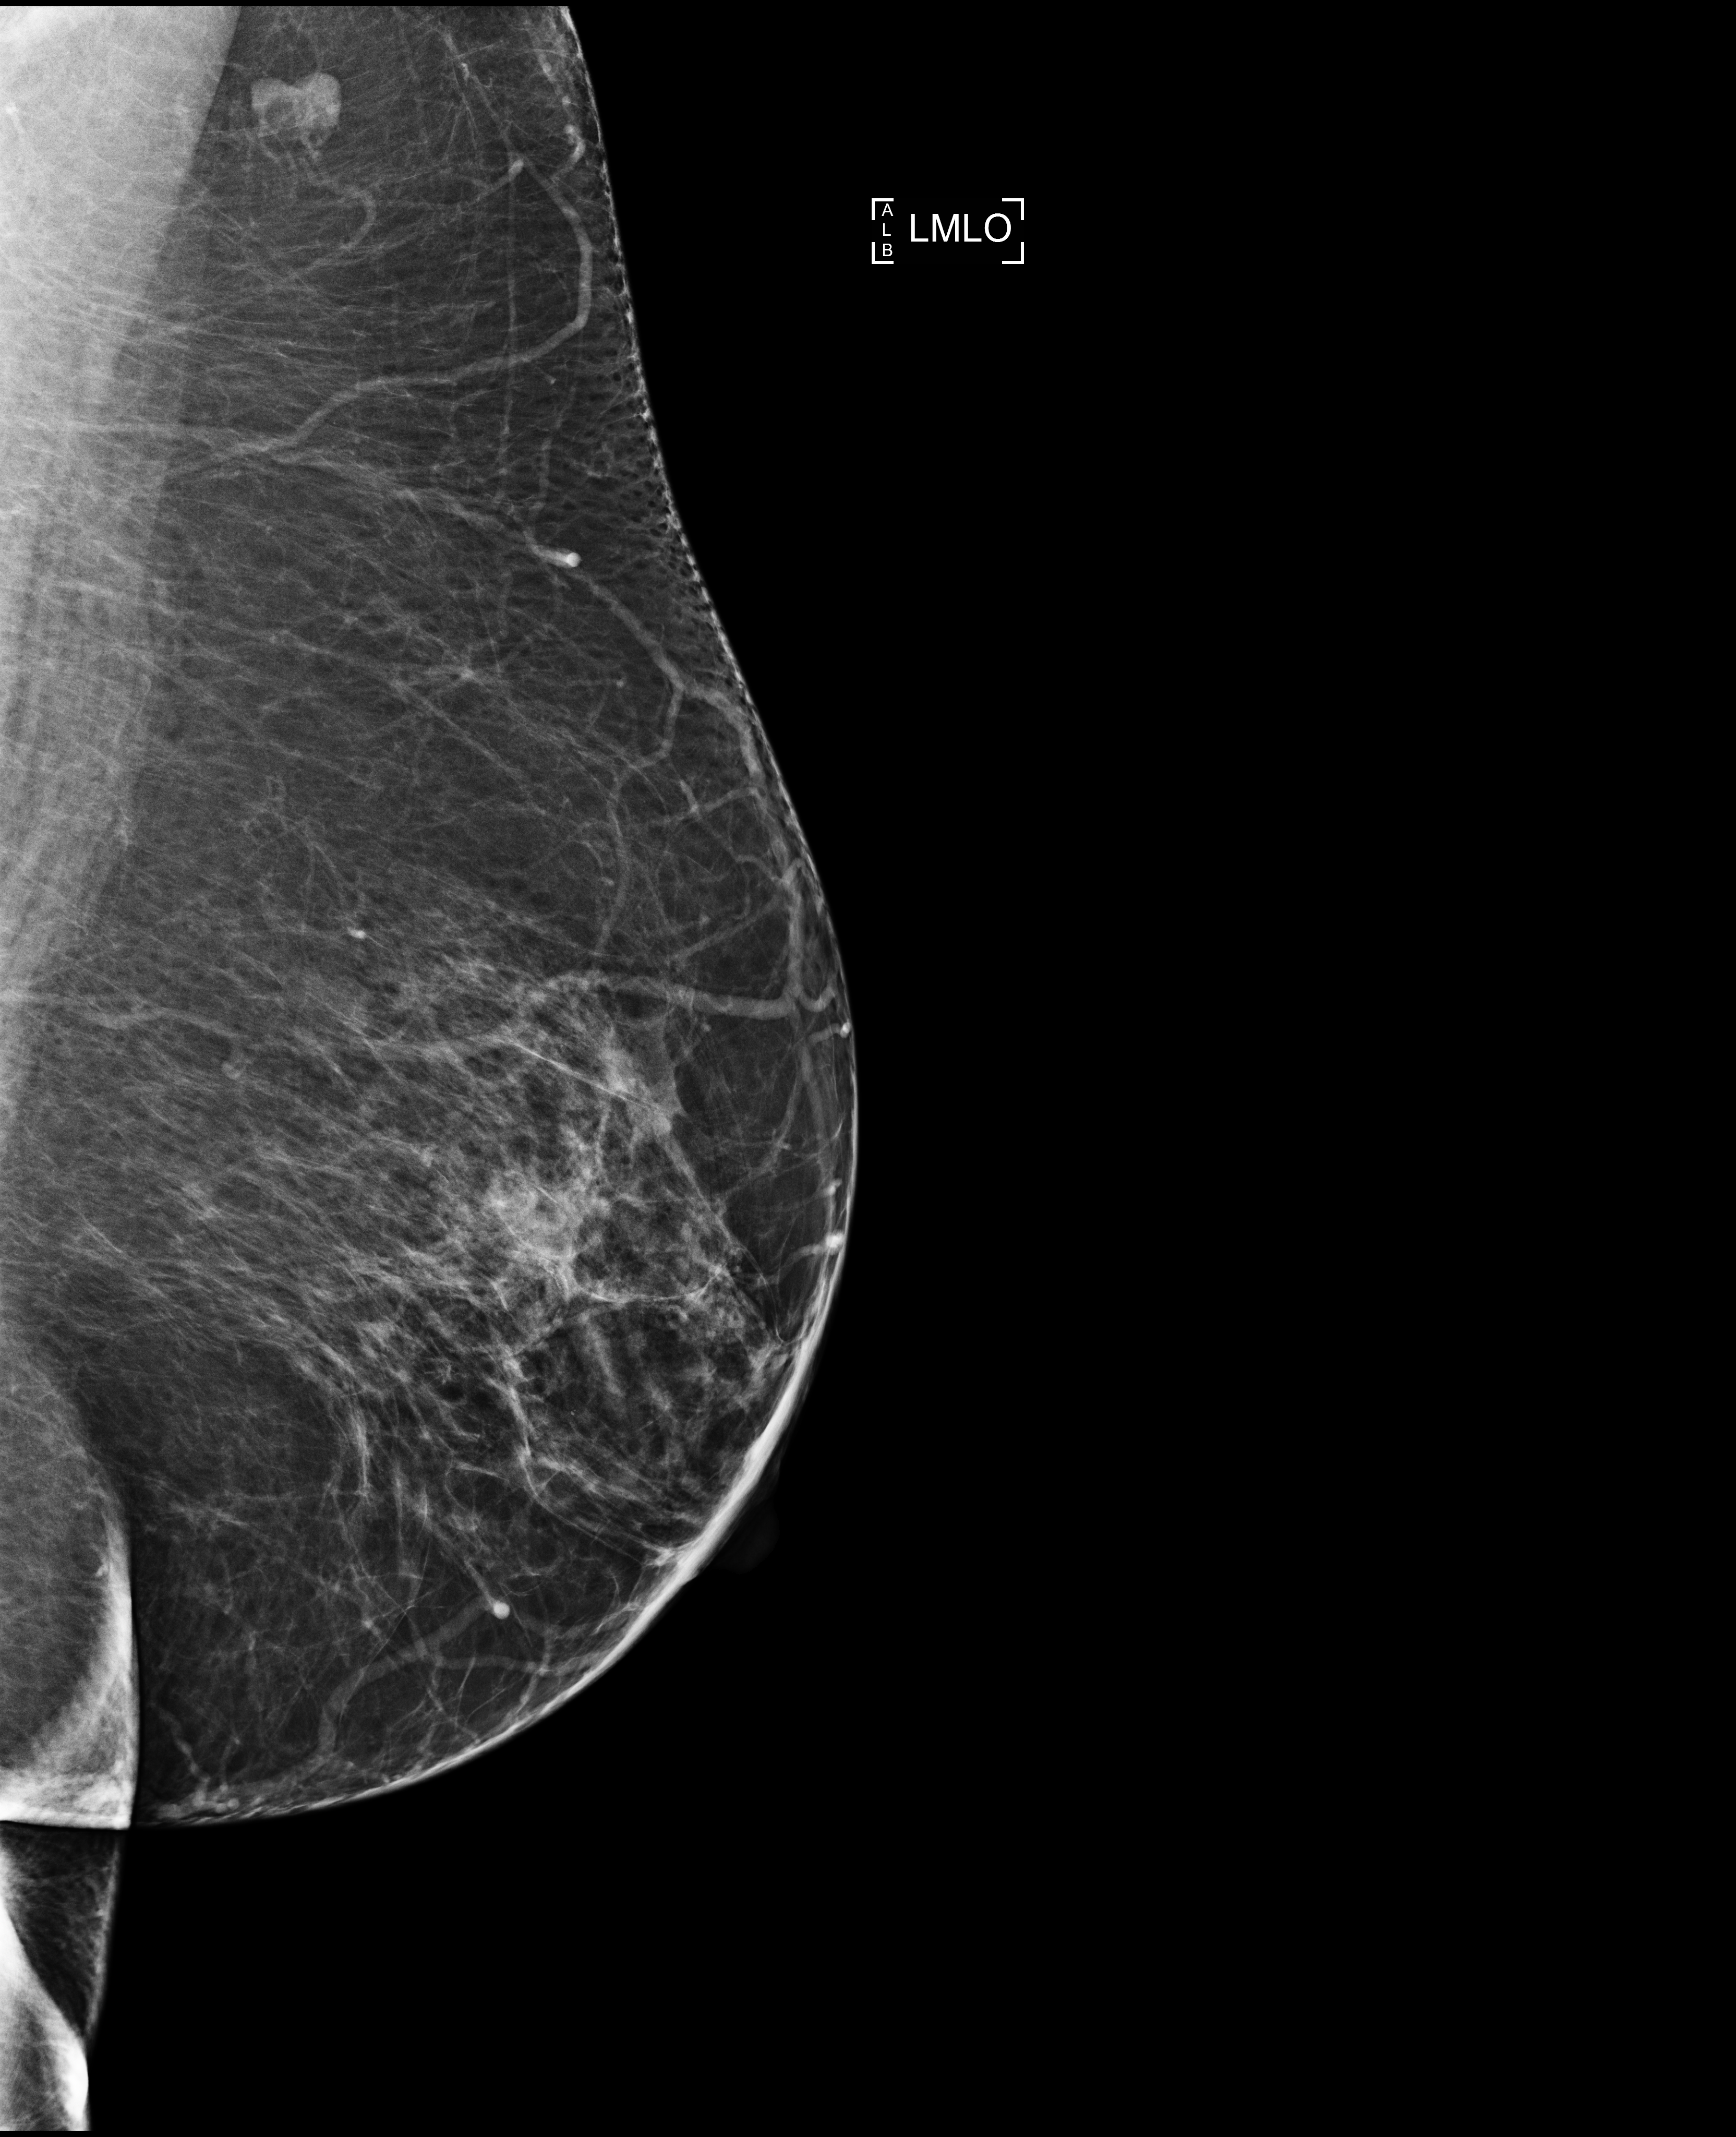
Screening examination. Patient: female, 62 years.
Image type: full-field digital mammogram. Breast: left. Projection: mediolateral oblique (MLO) view.